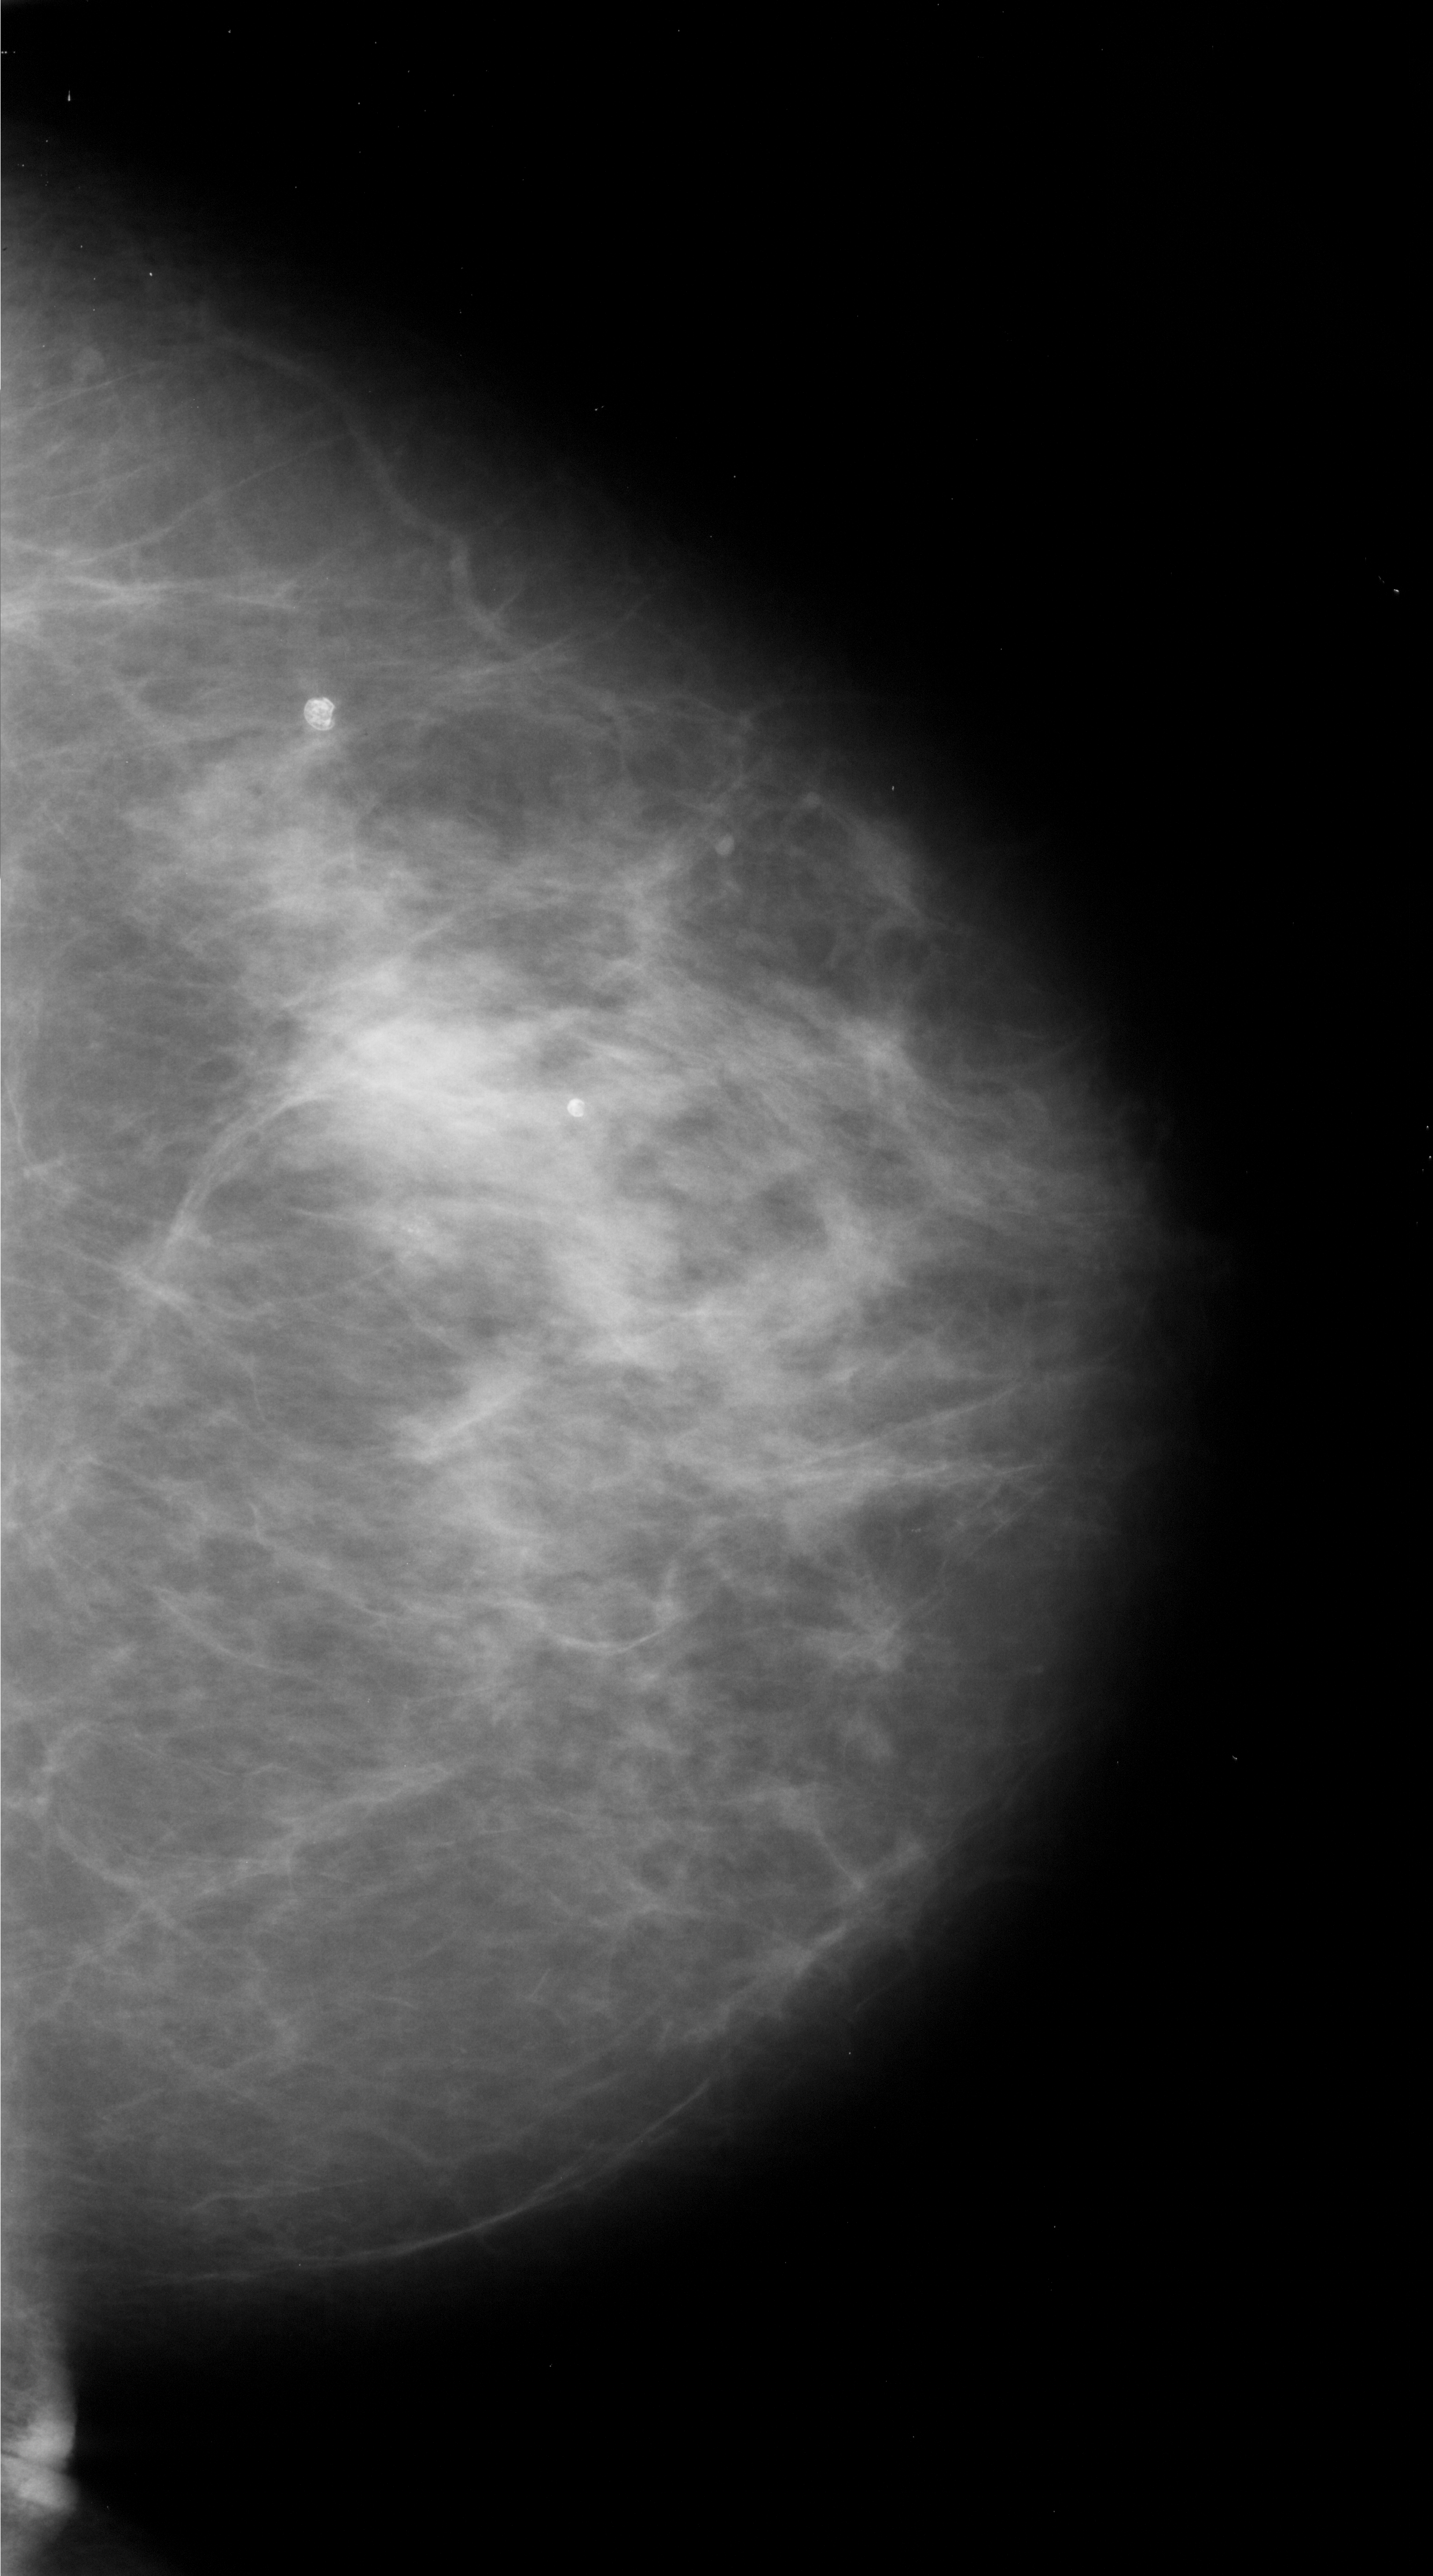
Digitized screen-film mammogram, right breast, CC view, breast composition: heterogeneously dense (BI-RADS density category 3 of 4).
Finding: calcifications, morphology pleomorphic, distribution linear; BI-RADS assessment category 4; subtlety rating 1 on a 1 (subtle) to 5 (obvious) scale; pathology (as recorded): malignant.